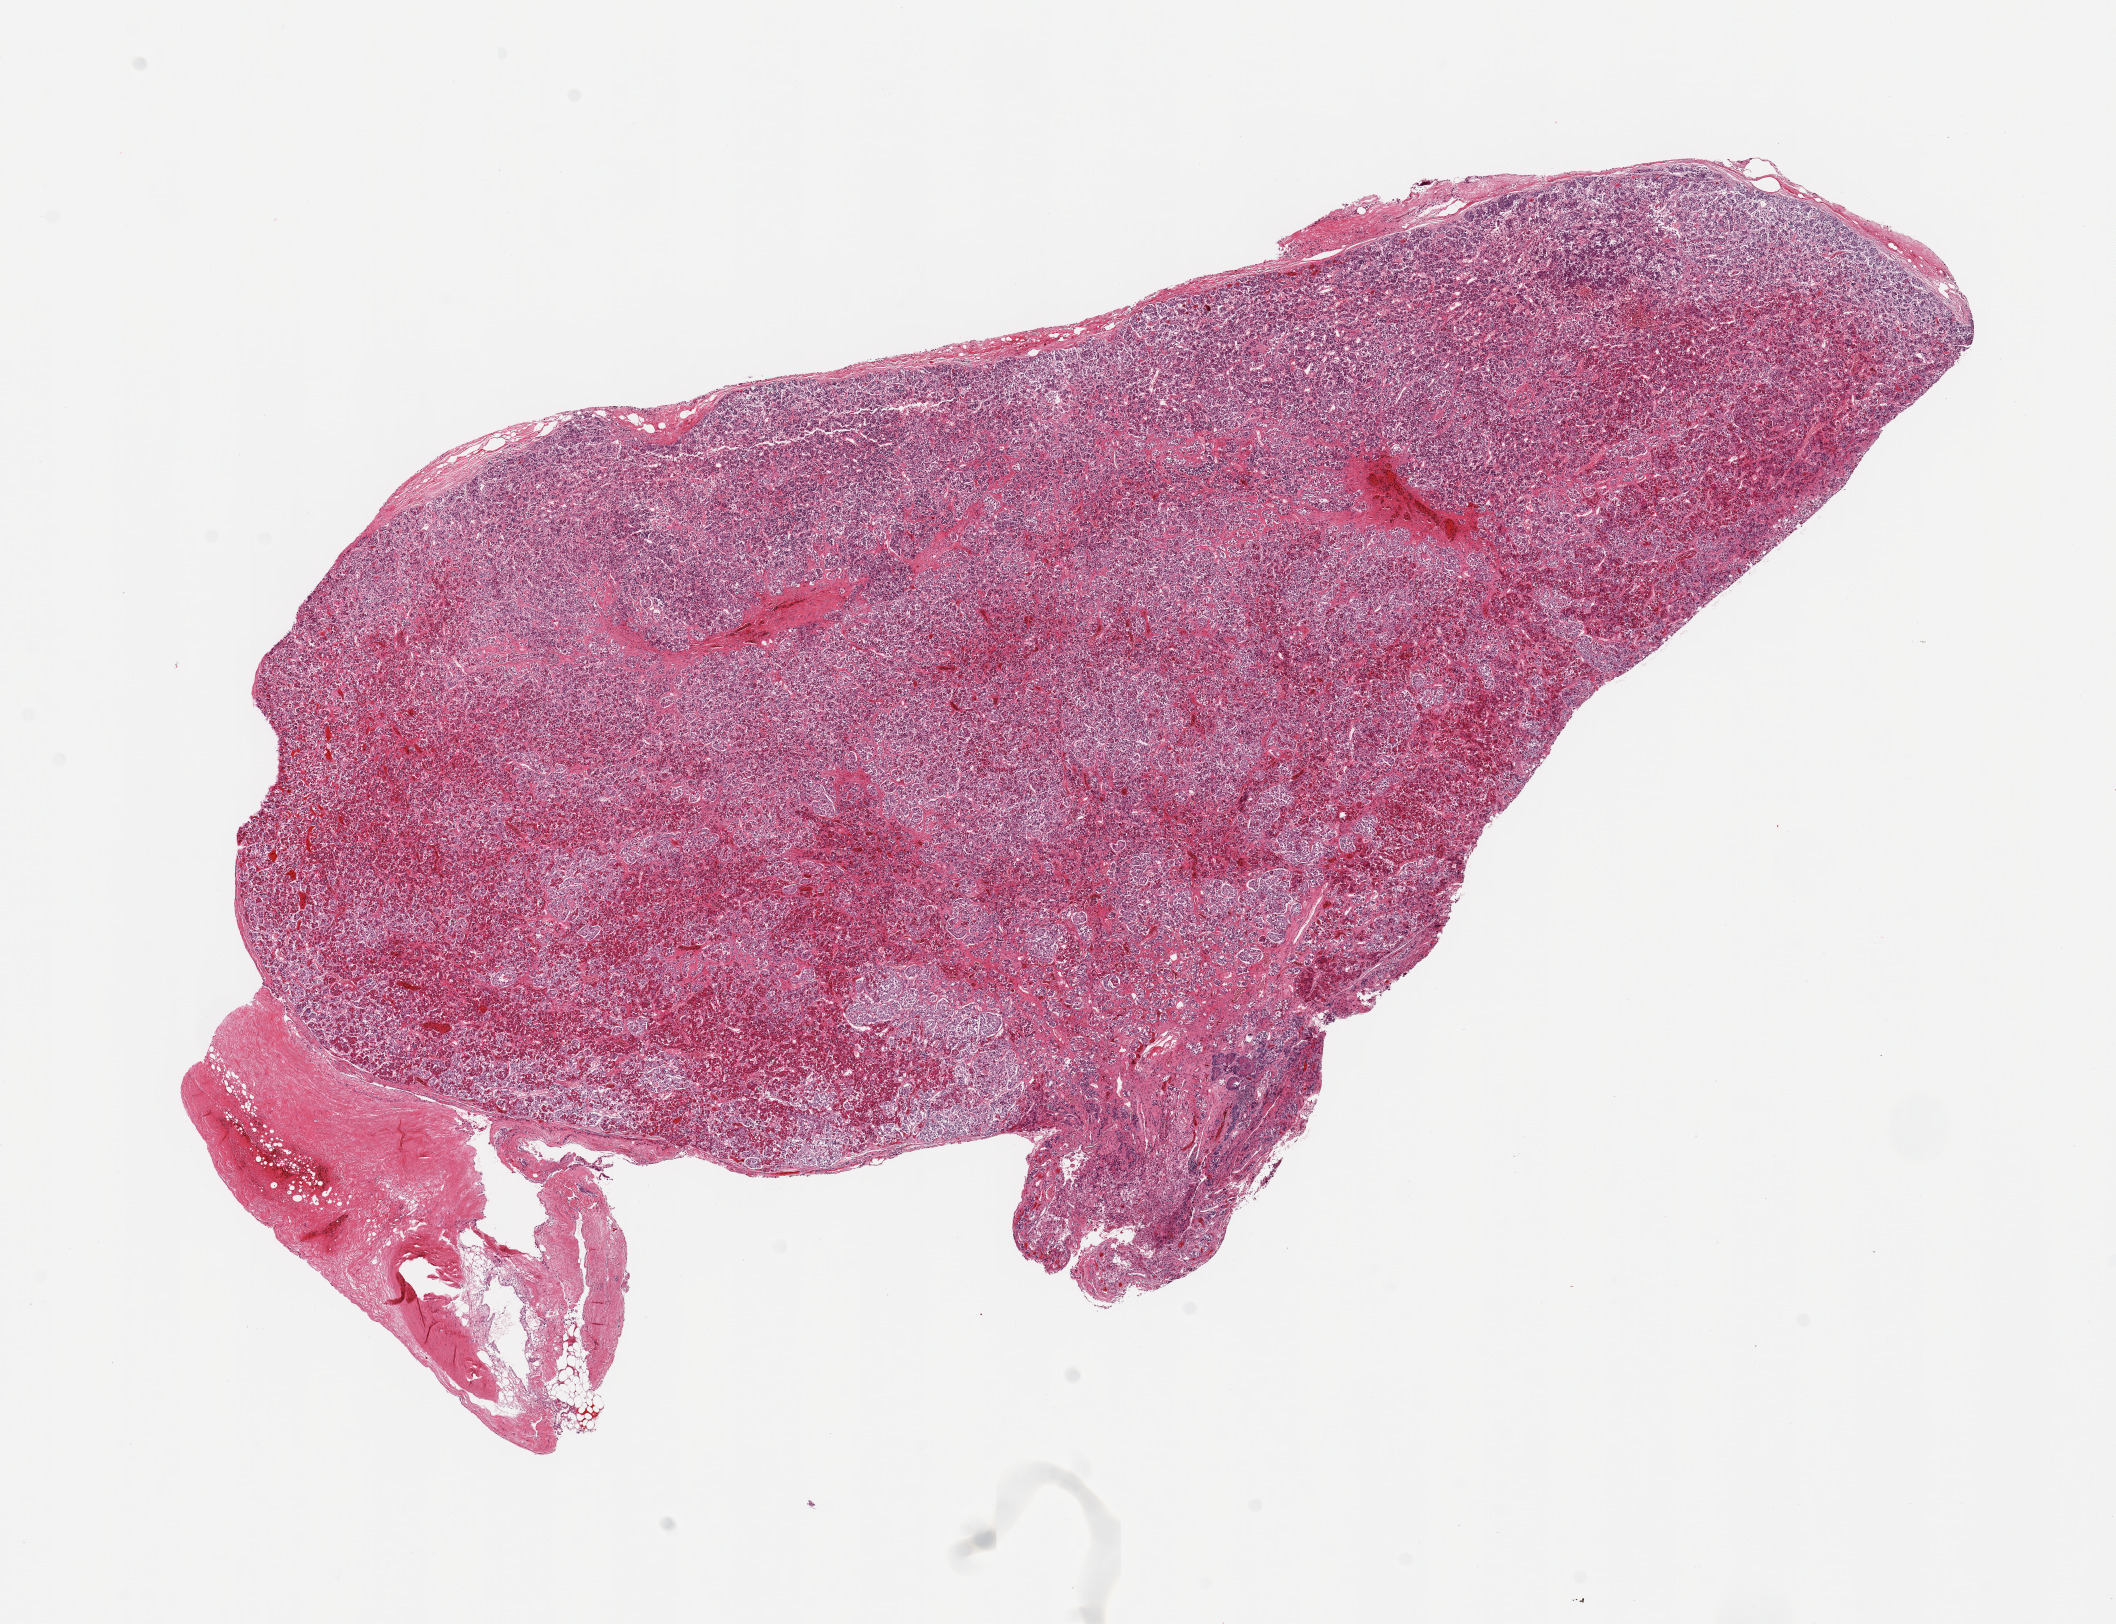
H&E whole-slide image, brightfield — a low-resolution overview of the entire scanned area, about 16.7 x 12.8 mm (acquisition: 20x scan); PAXgene-fixed, paraffin-embedded tissue; section of pituitary (target tissue); tissue donor sample. Donor sex: male.
Reviewer comment on this tissue sample: 1 pieces; adenohypophysis with few squamous nests.